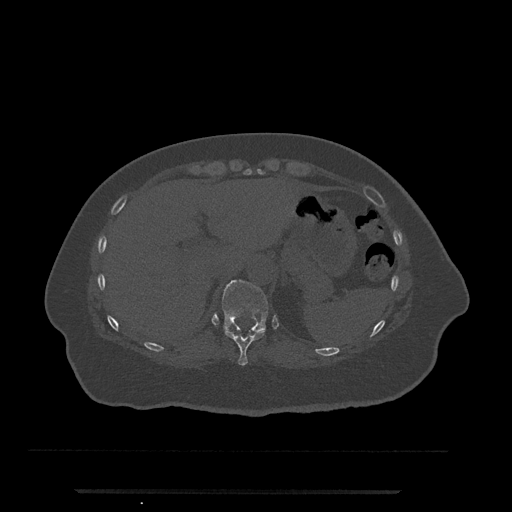
CT including the spine, one axial slice. Position 256 of 797 along the scan axis. Bone window (W 1800 / L 400 HU). 0.5 mm slice thickness. 512 × 512 image matrix, field of view 440 × 440 mm. Patient: female, 51 years. Case-level facts recorded for this patient, not image findings: primary cancer: neuro; vertebrae with lytic lesions (as recorded): T8.
Structures marked on this image (semi-automatically segmented with operator editing):
- T10 vertebra: bounding box [x1, y1, x2, y2] px = [224, 326, 266, 366]
- T11 vertebra: [222, 280, 268, 334]